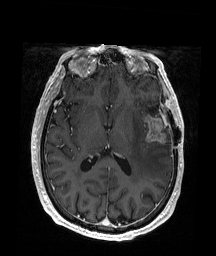
Brain MRI from a brain-tumour surgery series, one axial slice. Position 90 of 176 along the scan axis. T1-weighted post-contrast. 1 mm slice thickness. 216 × 256 image matrix, field of view 219 × 260 mm. Case-level facts recorded for this patient, not image findings: histopathology: Glioblastoma; WHO grade: 4; IDH mutation: no; tumour location: Left Frontal.
Structures marked on this image (expert manual segmentation):
- tumour: bounding box (x1, y1, x2, y2) in pixels: (144, 115, 166, 144)